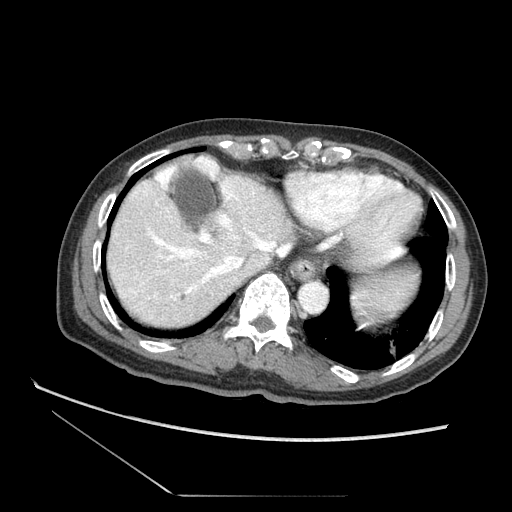
Contrast-enhanced abdominal CT (liver protocol), one axial slice; position 63 of 73 along the scan axis; reconstruction kernel STANDARD; 120 kVp; soft-tissue window (W 400 / L 40 HU); 2.5 mm slice thickness; 512 × 512 image matrix, field of view 360 × 360 mm. From the clinical record (not read from this slice): diagnosis: hepatocellular carcinoma (patient treated with transarterial chemoembolisation; whether this scan precedes or follows treatment is not stated here); TNM stage (as recorded): Stage-II; Child-Pugh class: A; tumour differentiation: moderately differentiated; tumour size: 3.8 cm.
Outlined on this slice (semi-automatic segmentation, software-assisted and operator-edited):
- abdominal aorta: box from (x=300, y=282) to (x=329, y=313) px
- liver parenchyma outside the tumour (the mass and vessels are separate outlines, so this box may not span the whole liver): (x=106, y=178)–(x=431, y=335)
- mass: (x=115, y=268)–(x=149, y=302)
- liver vessels: (x=165, y=239)–(x=219, y=273)